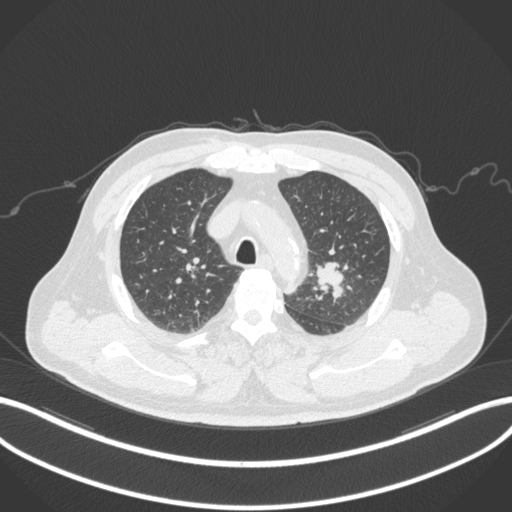
Chest CT, one axial slice; slice 230 of 286 in the series (ordered by position); reconstruction kernel B31f; lung window (W 1500 / L -600 HU); 1 mm slice thickness; 512 × 512 image matrix, field of view 400 × 400 mm. Male patient, age 67 years. Case-level facts recorded for this patient, not image findings: clinical TNM (as recorded): T2a N1 M0; histopathological grade: G3.
Outlined on this slice (rectangle marked by the reading radiologist):
- lung tumour (recorded histology: adenocarcinoma): box from (x=311, y=254) to (x=348, y=304) px